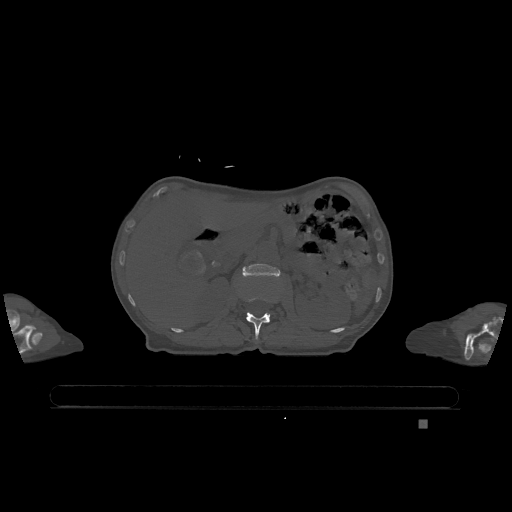
CT including the spine, one axial slice. Position 459 of 1317 along the scan axis. Bone window (W 1800 / L 400 HU). 0.5 mm slice thickness. 512 × 512 image matrix, field of view 500 × 500 mm. Patient: female, 74 years. Case-level facts recorded for this patient, not image findings: primary cancer: lung; vertebrae with lytic lesions (as recorded): T1, T4, T5, T6, L4, L5.
Structures marked on this image (semi-automatic segmentation, software-assisted and operator-edited):
- L1 vertebra: bounding box <245,297,270,339> (left, top, right, bottom; pixels)
- L2 vertebra: <243,264,280,277>